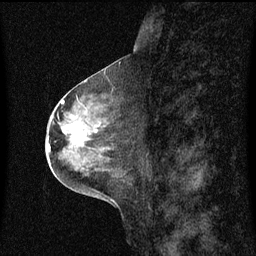
Breast MRI (dynamic contrast-enhanced), one sagittal slice; position 31 of 60 along the scan axis; dynamic contrast-enhanced series, image 2 of 3 at this slice position (ordered by acquisition); 1.5 T; TE 4.2 ms, TR 8.4 ms; 2 mm slice thickness; 256 × 256 image matrix, field of view 200 × 200 mm. Patient: female, 49 years. From the clinical record (not read from this slice): setting: breast cancer imaged before/during neoadjuvant chemotherapy; receptor status: HR-positive, HER2-negative.
Outlined on this slice (semi-automatically segmented with operator editing):
- analysis volume of interest (the breast-tissue region the enhancement analysis was run in; not a lesion): box from (x=59, y=101) to (x=115, y=158) px
- tumour enhancement mask (voxels above the 70 % enhancement threshold inside the analysis volume of interest): (x=63, y=128)–(x=97, y=141)